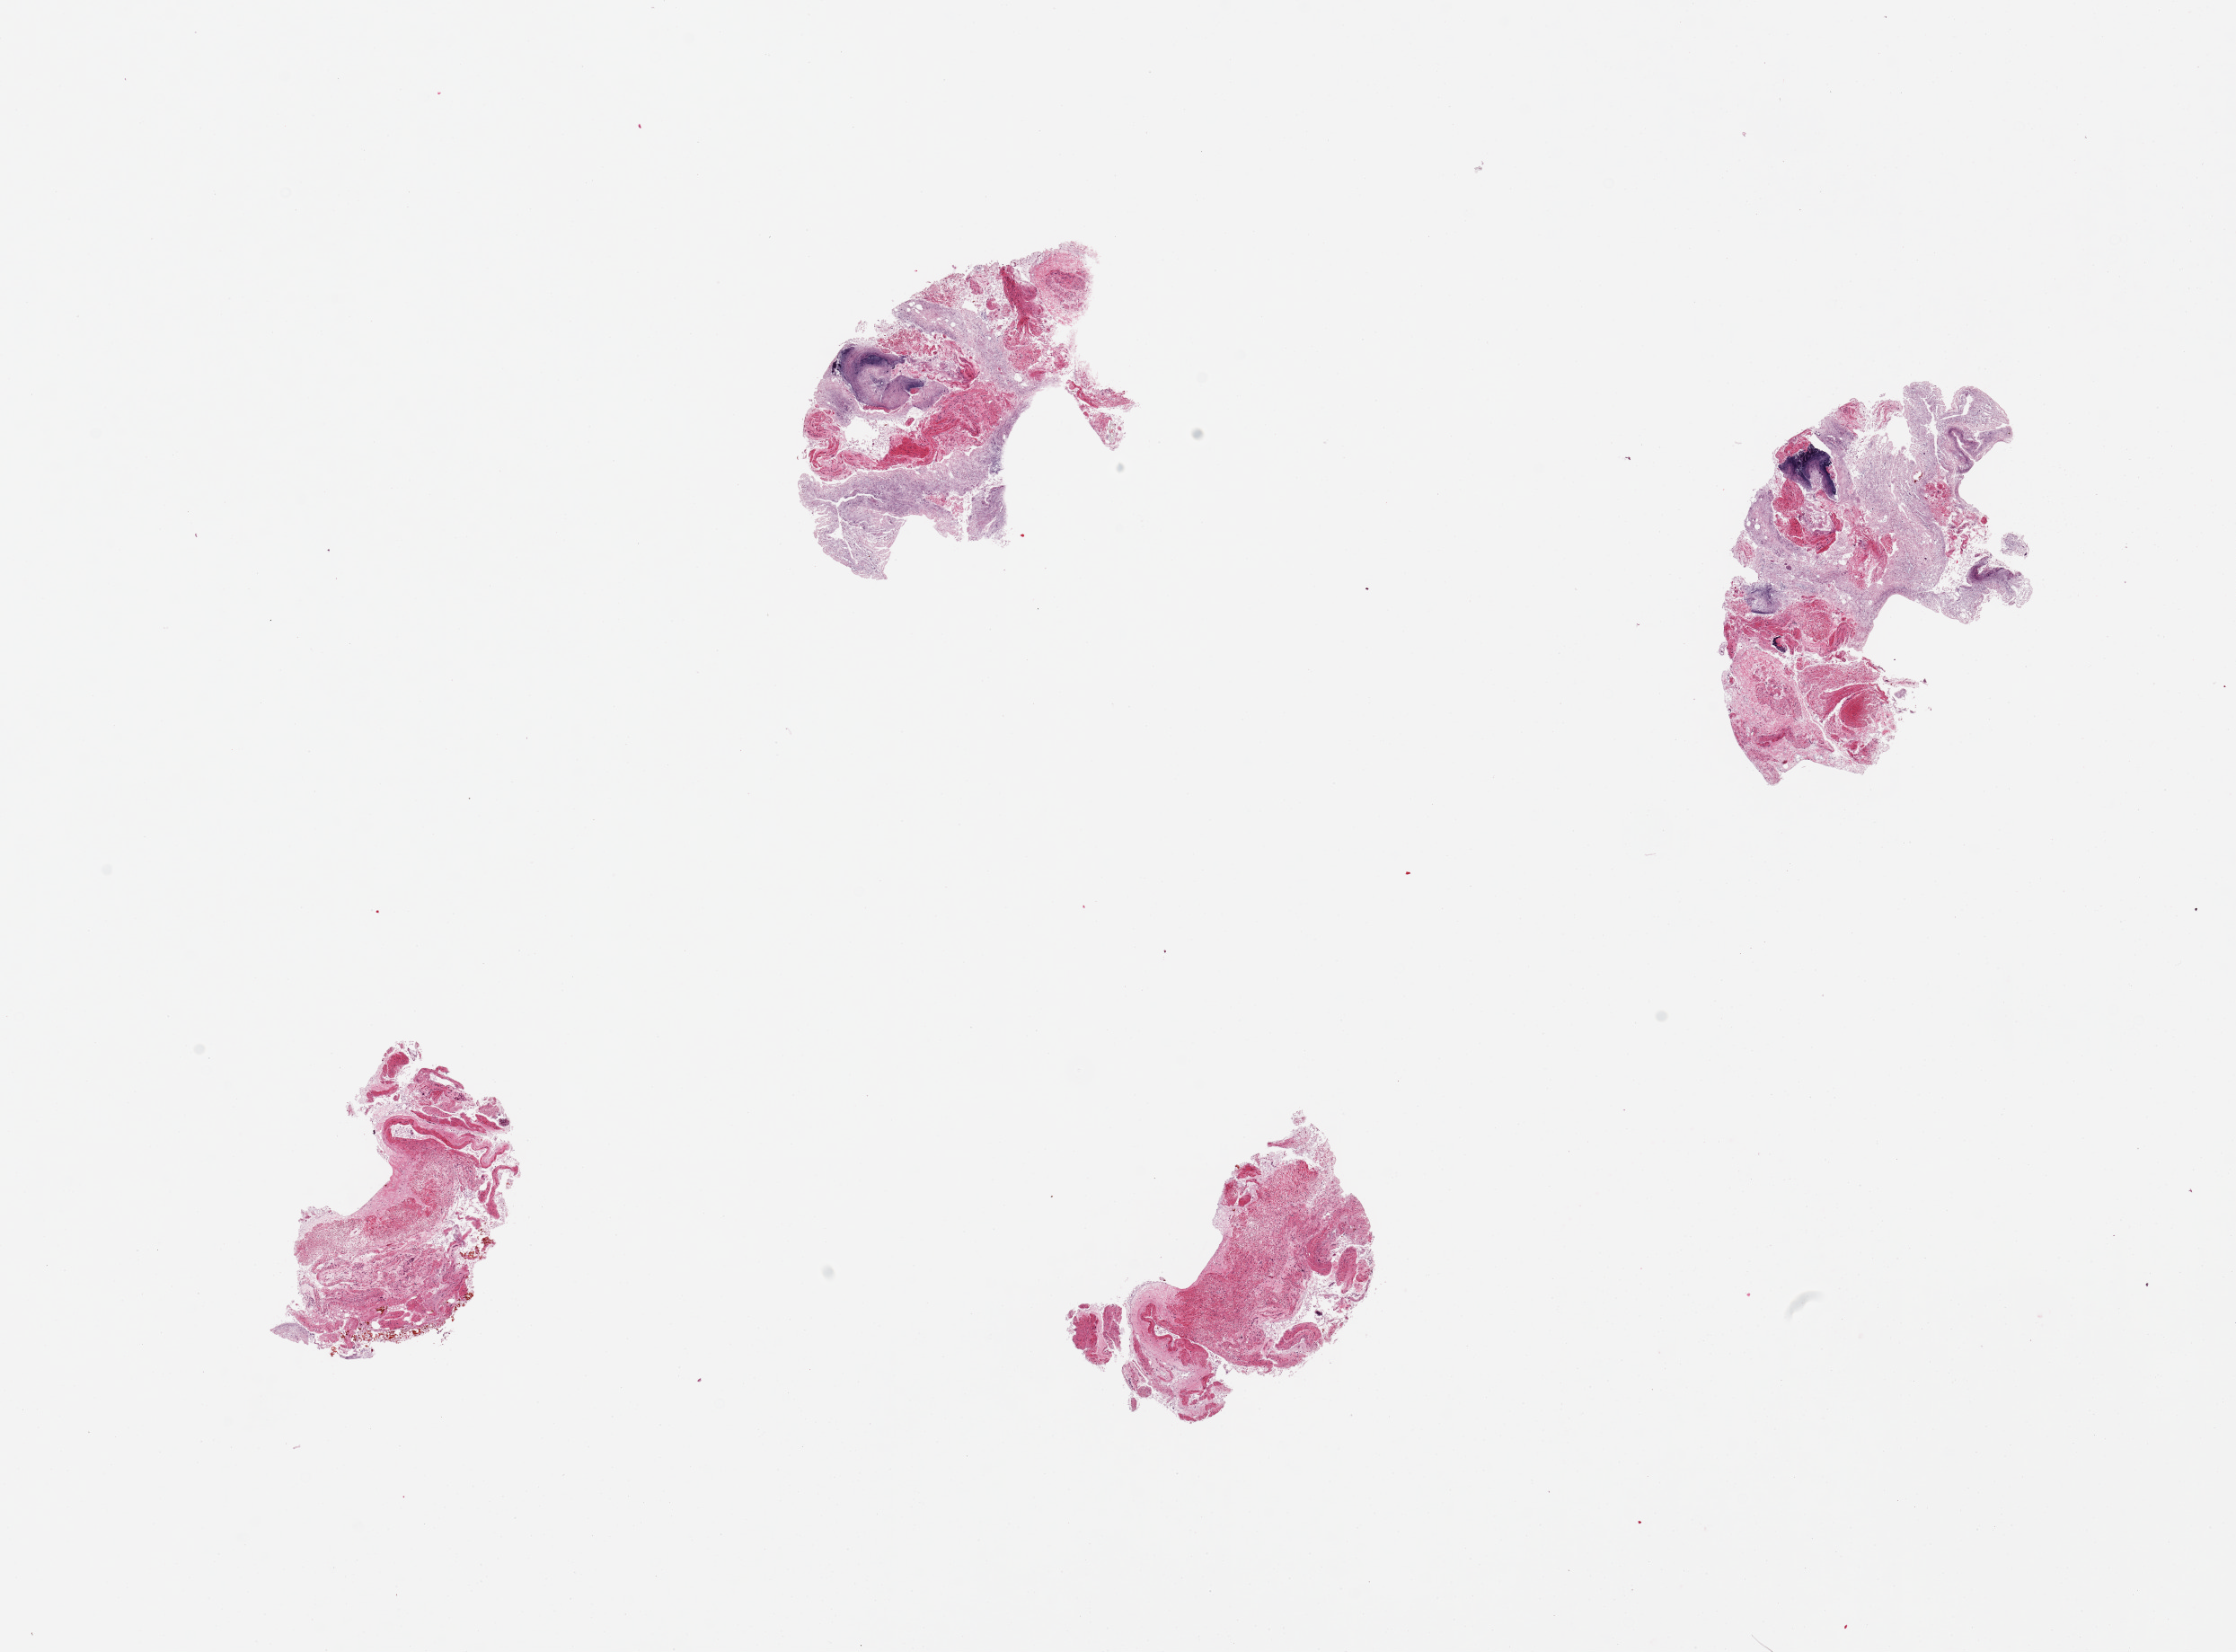
Hematoxylin and eosin (H&E) whole-slide image, brightfield — whole scanned area (about 19.7 x 14.5 mm, slide scanned at 20x) shown as a low-resolution overview, PAXgene-fixed, paraffin-embedded tissue, sampled site (target tissue): ileum, donor tissue sample. Donor sex: female.
Review note (as recorded): 4 pieces, mucosa totally autolyzed; ~5-10% specimen is lymphoid aggregates.